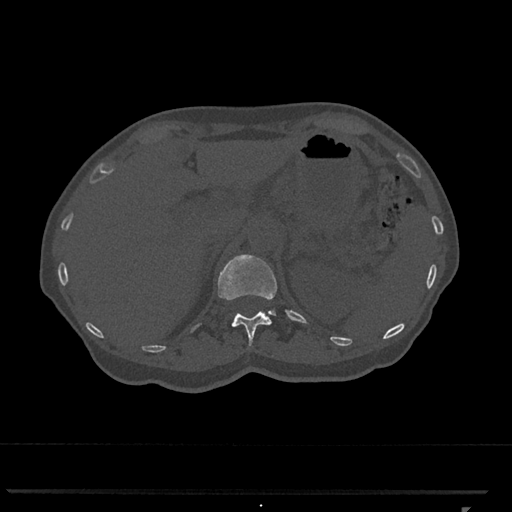
CT including the spine, one axial slice. Slice 452 of 793 in the series (ordered by position). Reconstruction kernel Br40s/3. 120 kVp. Bone window (W 1800 / L 400 HU). 0.5 mm slice thickness. 512 × 512 image matrix, field of view 380 × 380 mm. Female patient, age 62 years. Case-level facts recorded for this patient, not image findings: primary cancer: renal.
Outlined on this slice (semi-automatically segmented with operator editing):
- T12 vertebra: box from (x=218, y=254) to (x=277, y=346) px